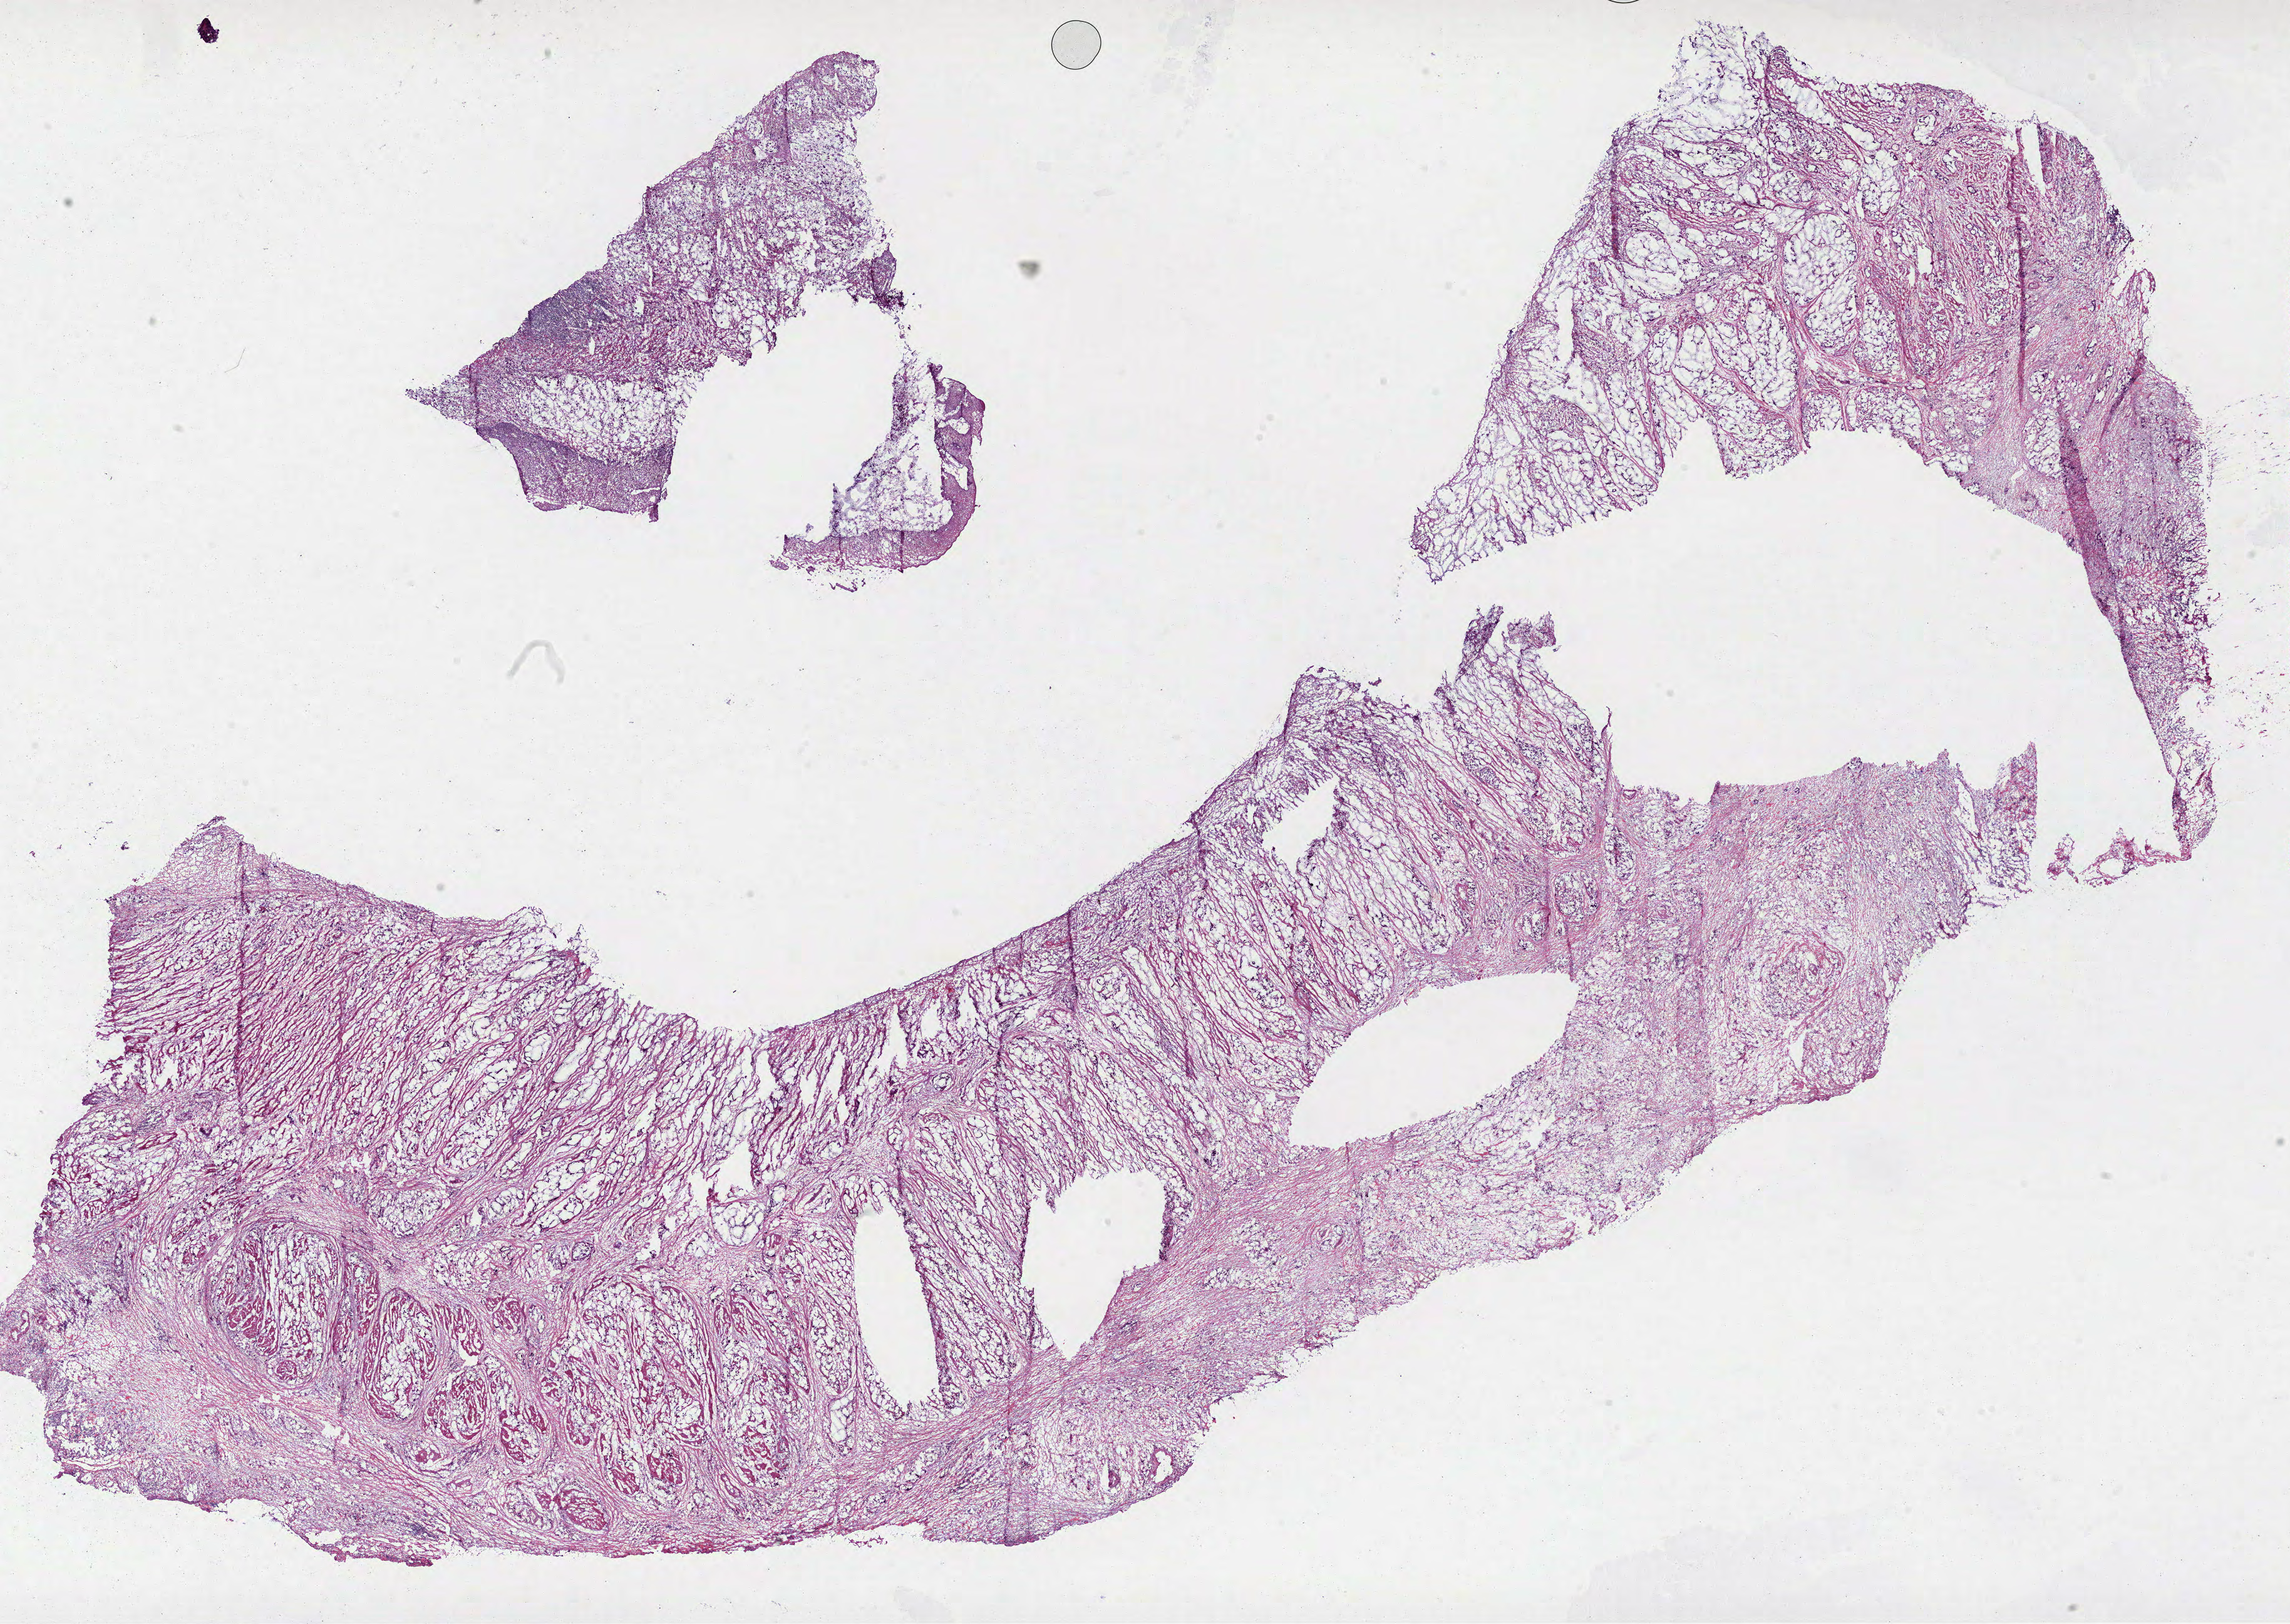
Hematoxylin and eosin (H&E) stained whole-slide image, whole scanned area (about 29.5 x 20.9 mm) shown as a low-resolution overview; frozen section; primary tumour sample from the stomach. Male patient; age at initial diagnosis 59 years. Histologic grade: G3 (poorly differentiated). Slide review estimates, as recorded: tumour cells 68%, tumour nuclei 70%, normal cells 2%, stromal cells 30%, necrosis 0%.
Lymph nodes positive (case pathology): 1 of 7 examined. Diagnosis: Mucinous adenocarcinoma (cardia, NOS). AJCC pathologic stage: IIIA (7th edition).